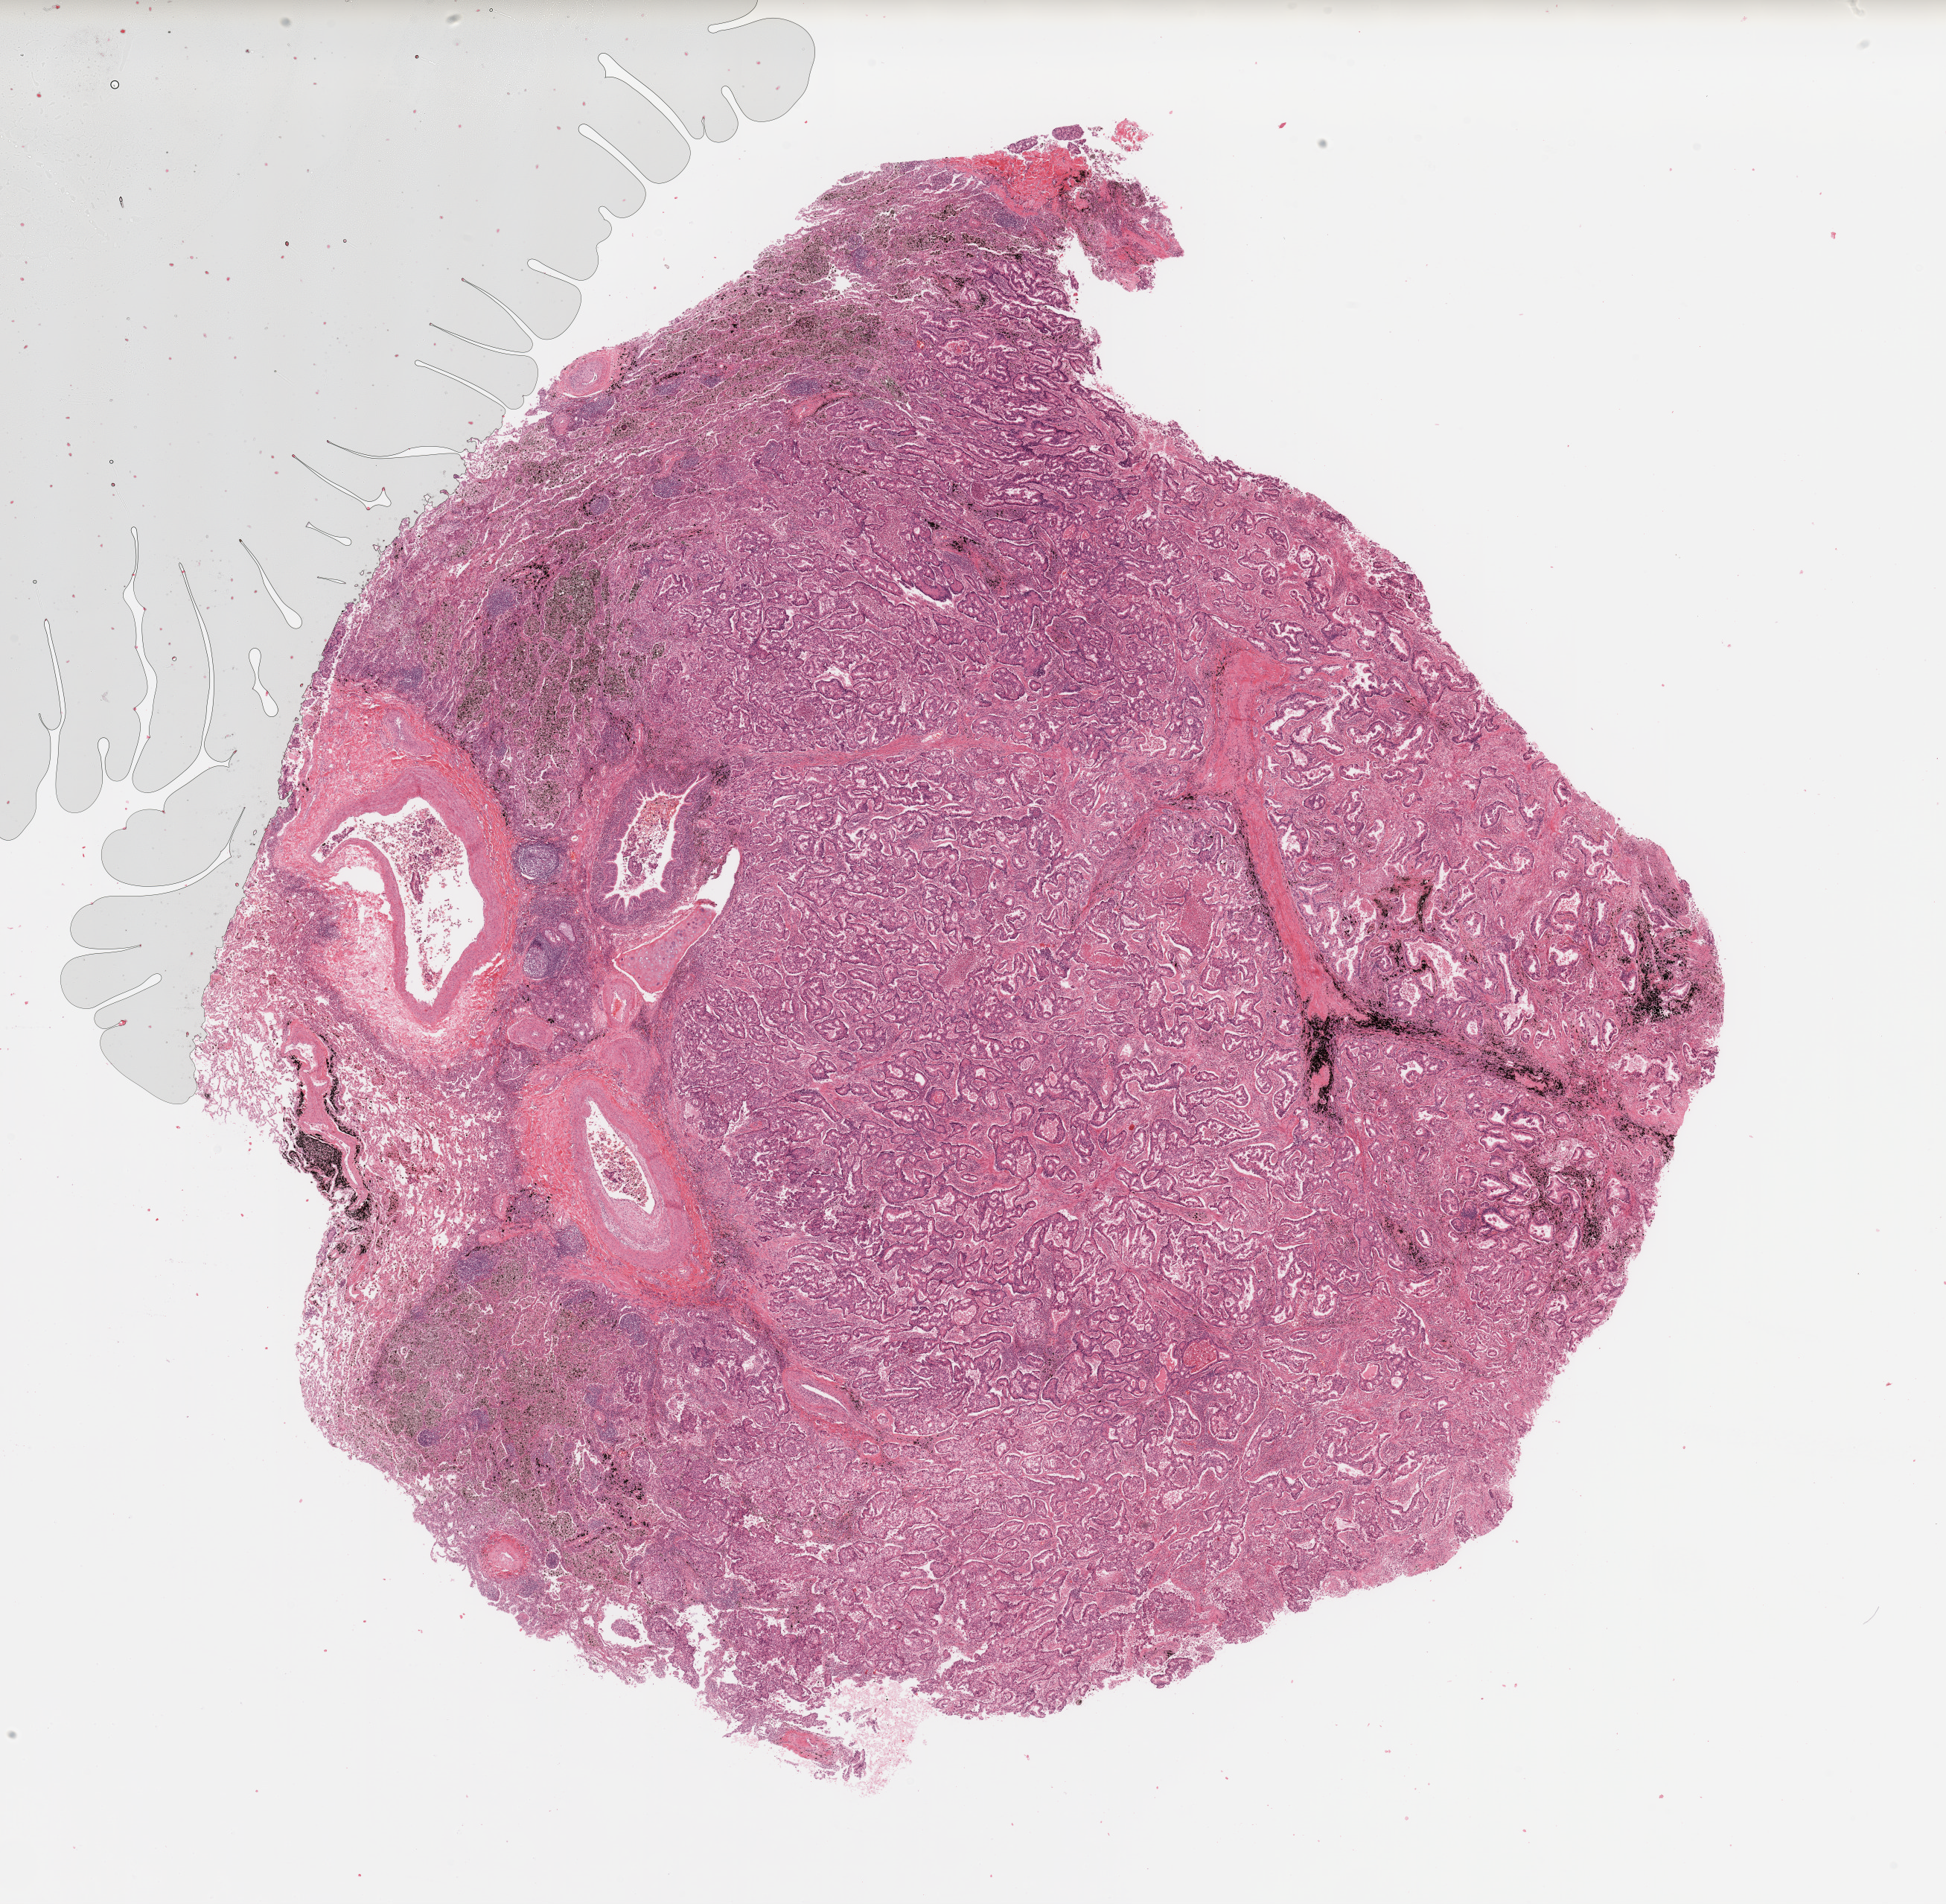
Digitized H&E tissue section (whole slide) — shown as a low-resolution overview of the whole scanned area (about 20.7 x 20.2 mm). Tumour tissue sample, sampled site: lung. Male, 60 y/o. Histologic grade: G2 (moderately differentiated). Pathologist review of this section (percent, as recorded): tumour nuclei 80%, necrosis 10%.
Diagnosis: Adenocarcinoma, NOS. AJCC pathologic stage: IIA.